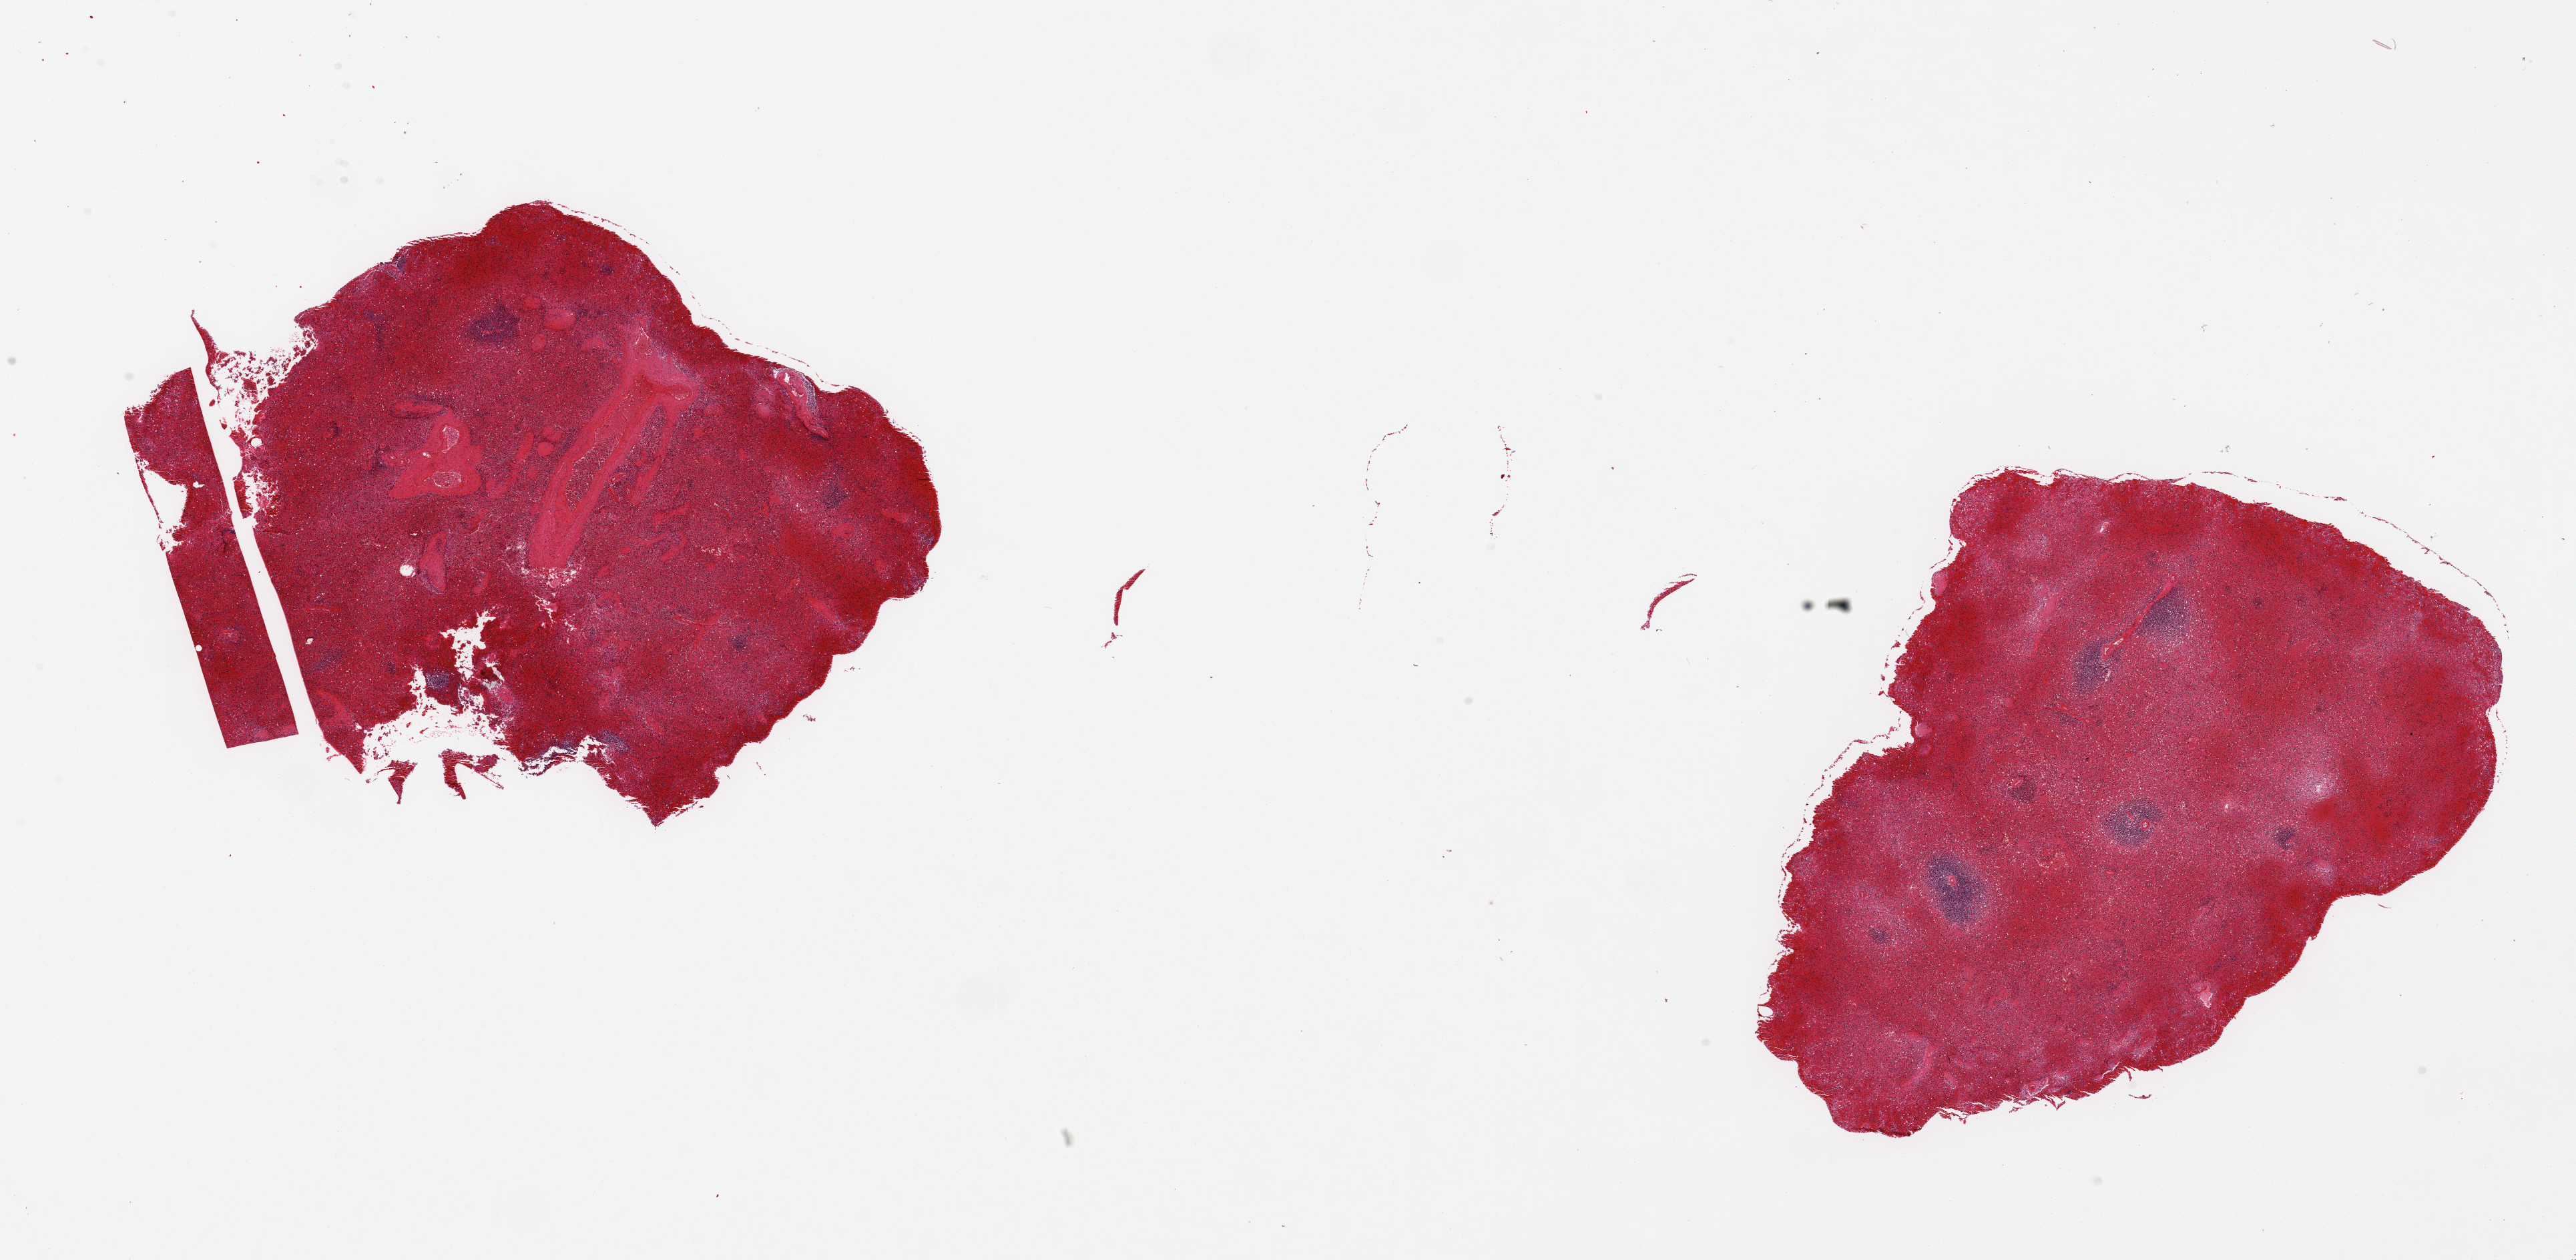
H&E whole-slide image — low-resolution overview of the scanned area, about 30.5 x 14.9 mm; PAXgene-fixed paraffin-embedded (PFPE) section; section of spleen (target tissue); tissue donor sample. Donor sex: male.
Reviewer comment on this tissue sample: 2 pieces ~8x6mm, severe red pulp congestion.